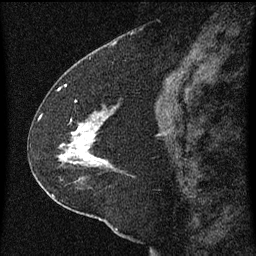
Breast MRI (dynamic contrast-enhanced), one sagittal slice; position 30 of 60 along the scan axis; dynamic contrast-enhanced series, image 2 of 3 at this slice position (ordered by acquisition); 1.5 T; TE 4.2 ms, TR 8 ms; 2 mm slice thickness; 256 × 256 image matrix, field of view 180 × 180 mm. Female patient, age 47 years.
Outlined on this slice (semi-automatically segmented with operator editing):
- analysis volume of interest (the breast-tissue region the enhancement analysis was run in; not a lesion): box from (x=36, y=96) to (x=120, y=213) px
- tumour enhancement mask (voxels above the 70 % enhancement threshold inside the analysis volume of interest): (x=59, y=116)–(x=104, y=167)